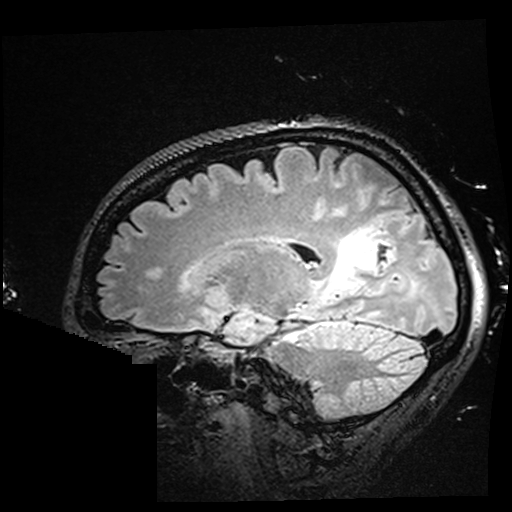
Brain MRI from a brain-tumour surgery series, one sagittal slice; slice 109 of 176 in the series (ordered by position); T2 FLAIR; 1 mm slice thickness; 512 × 512 image matrix, field of view 250 × 250 mm. Case-level facts recorded for this patient, not image findings: histopathology: Oligodendroglioma; WHO grade: 2.
Annotated regions visible in this slice (outlined manually by an expert reader):
- residual tumour: bounding box (x1, y1, x2, y2) in pixels: (323, 229, 385, 295)